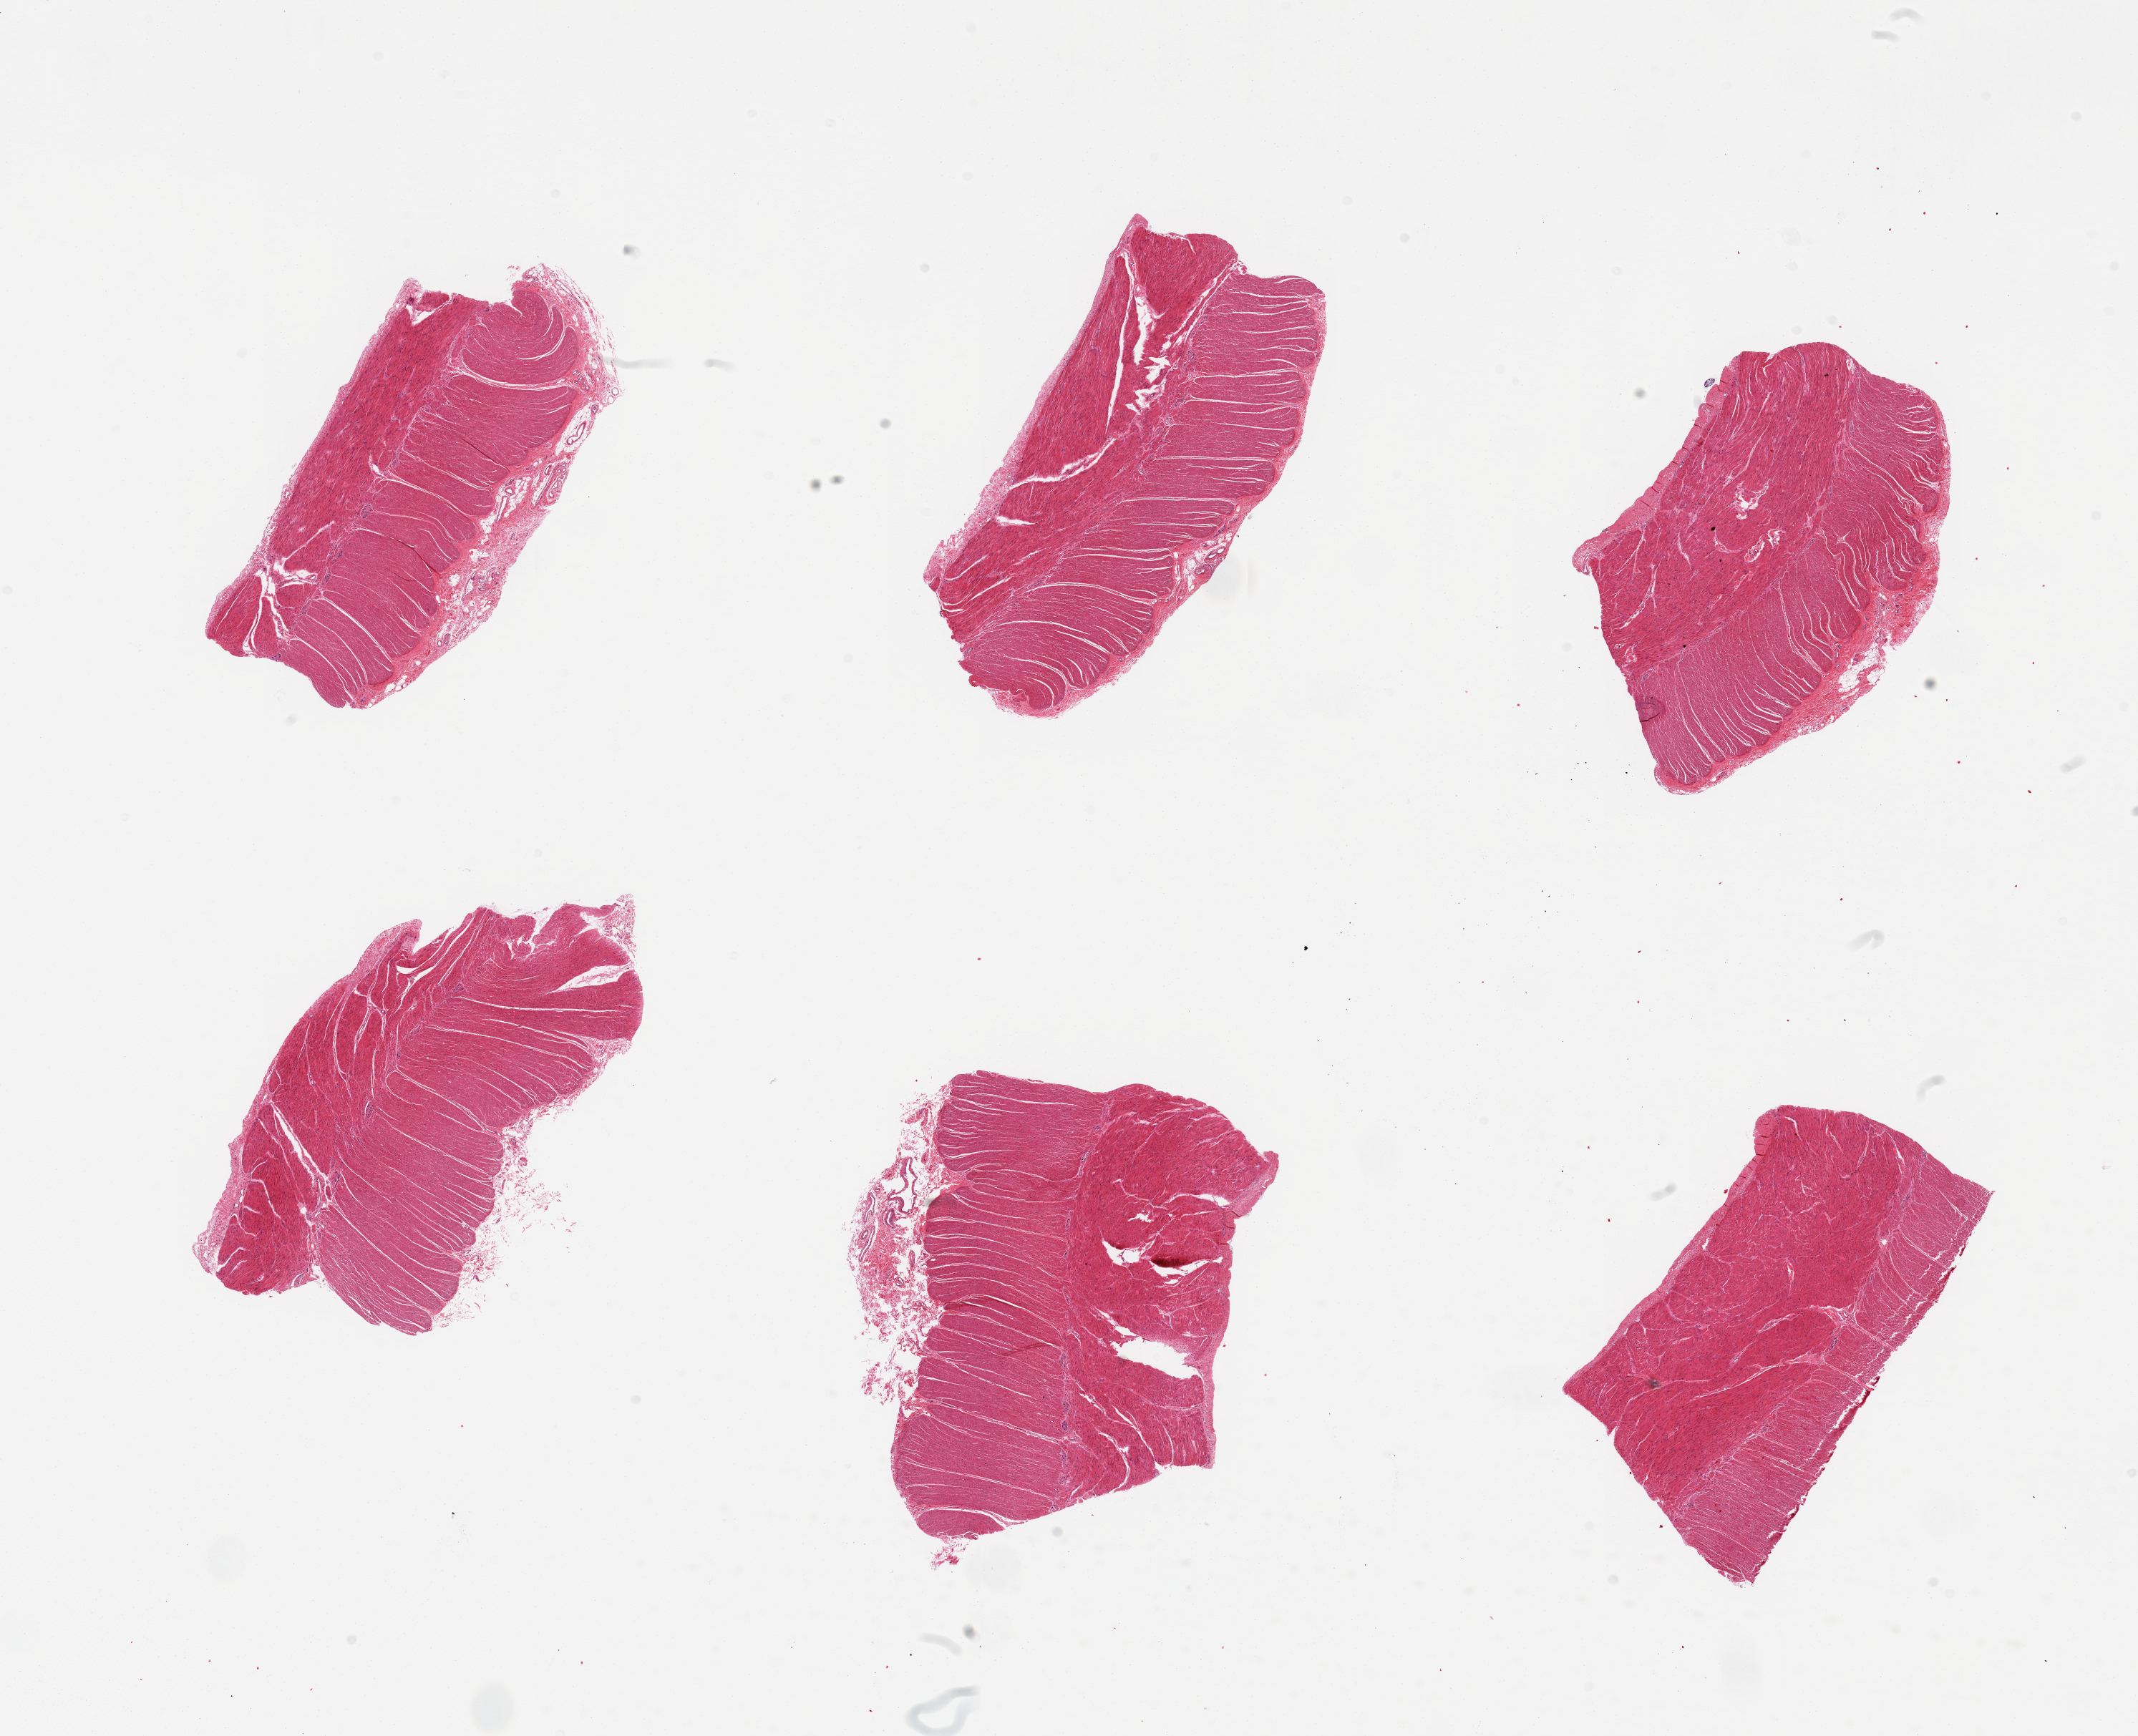
Haematoxylin and eosin whole-slide image, brightfield — a low-resolution overview of the entire scanned area, about 23.6 x 19.2 mm (slide scanned at 20x), PAXgene-fixed paraffin-embedded (PFPE) section, sampled site (target tissue): sigmoid colon, donor tissue sample. Donor sex: male.
- review note (as recorded): 6 pieces, well trimmed